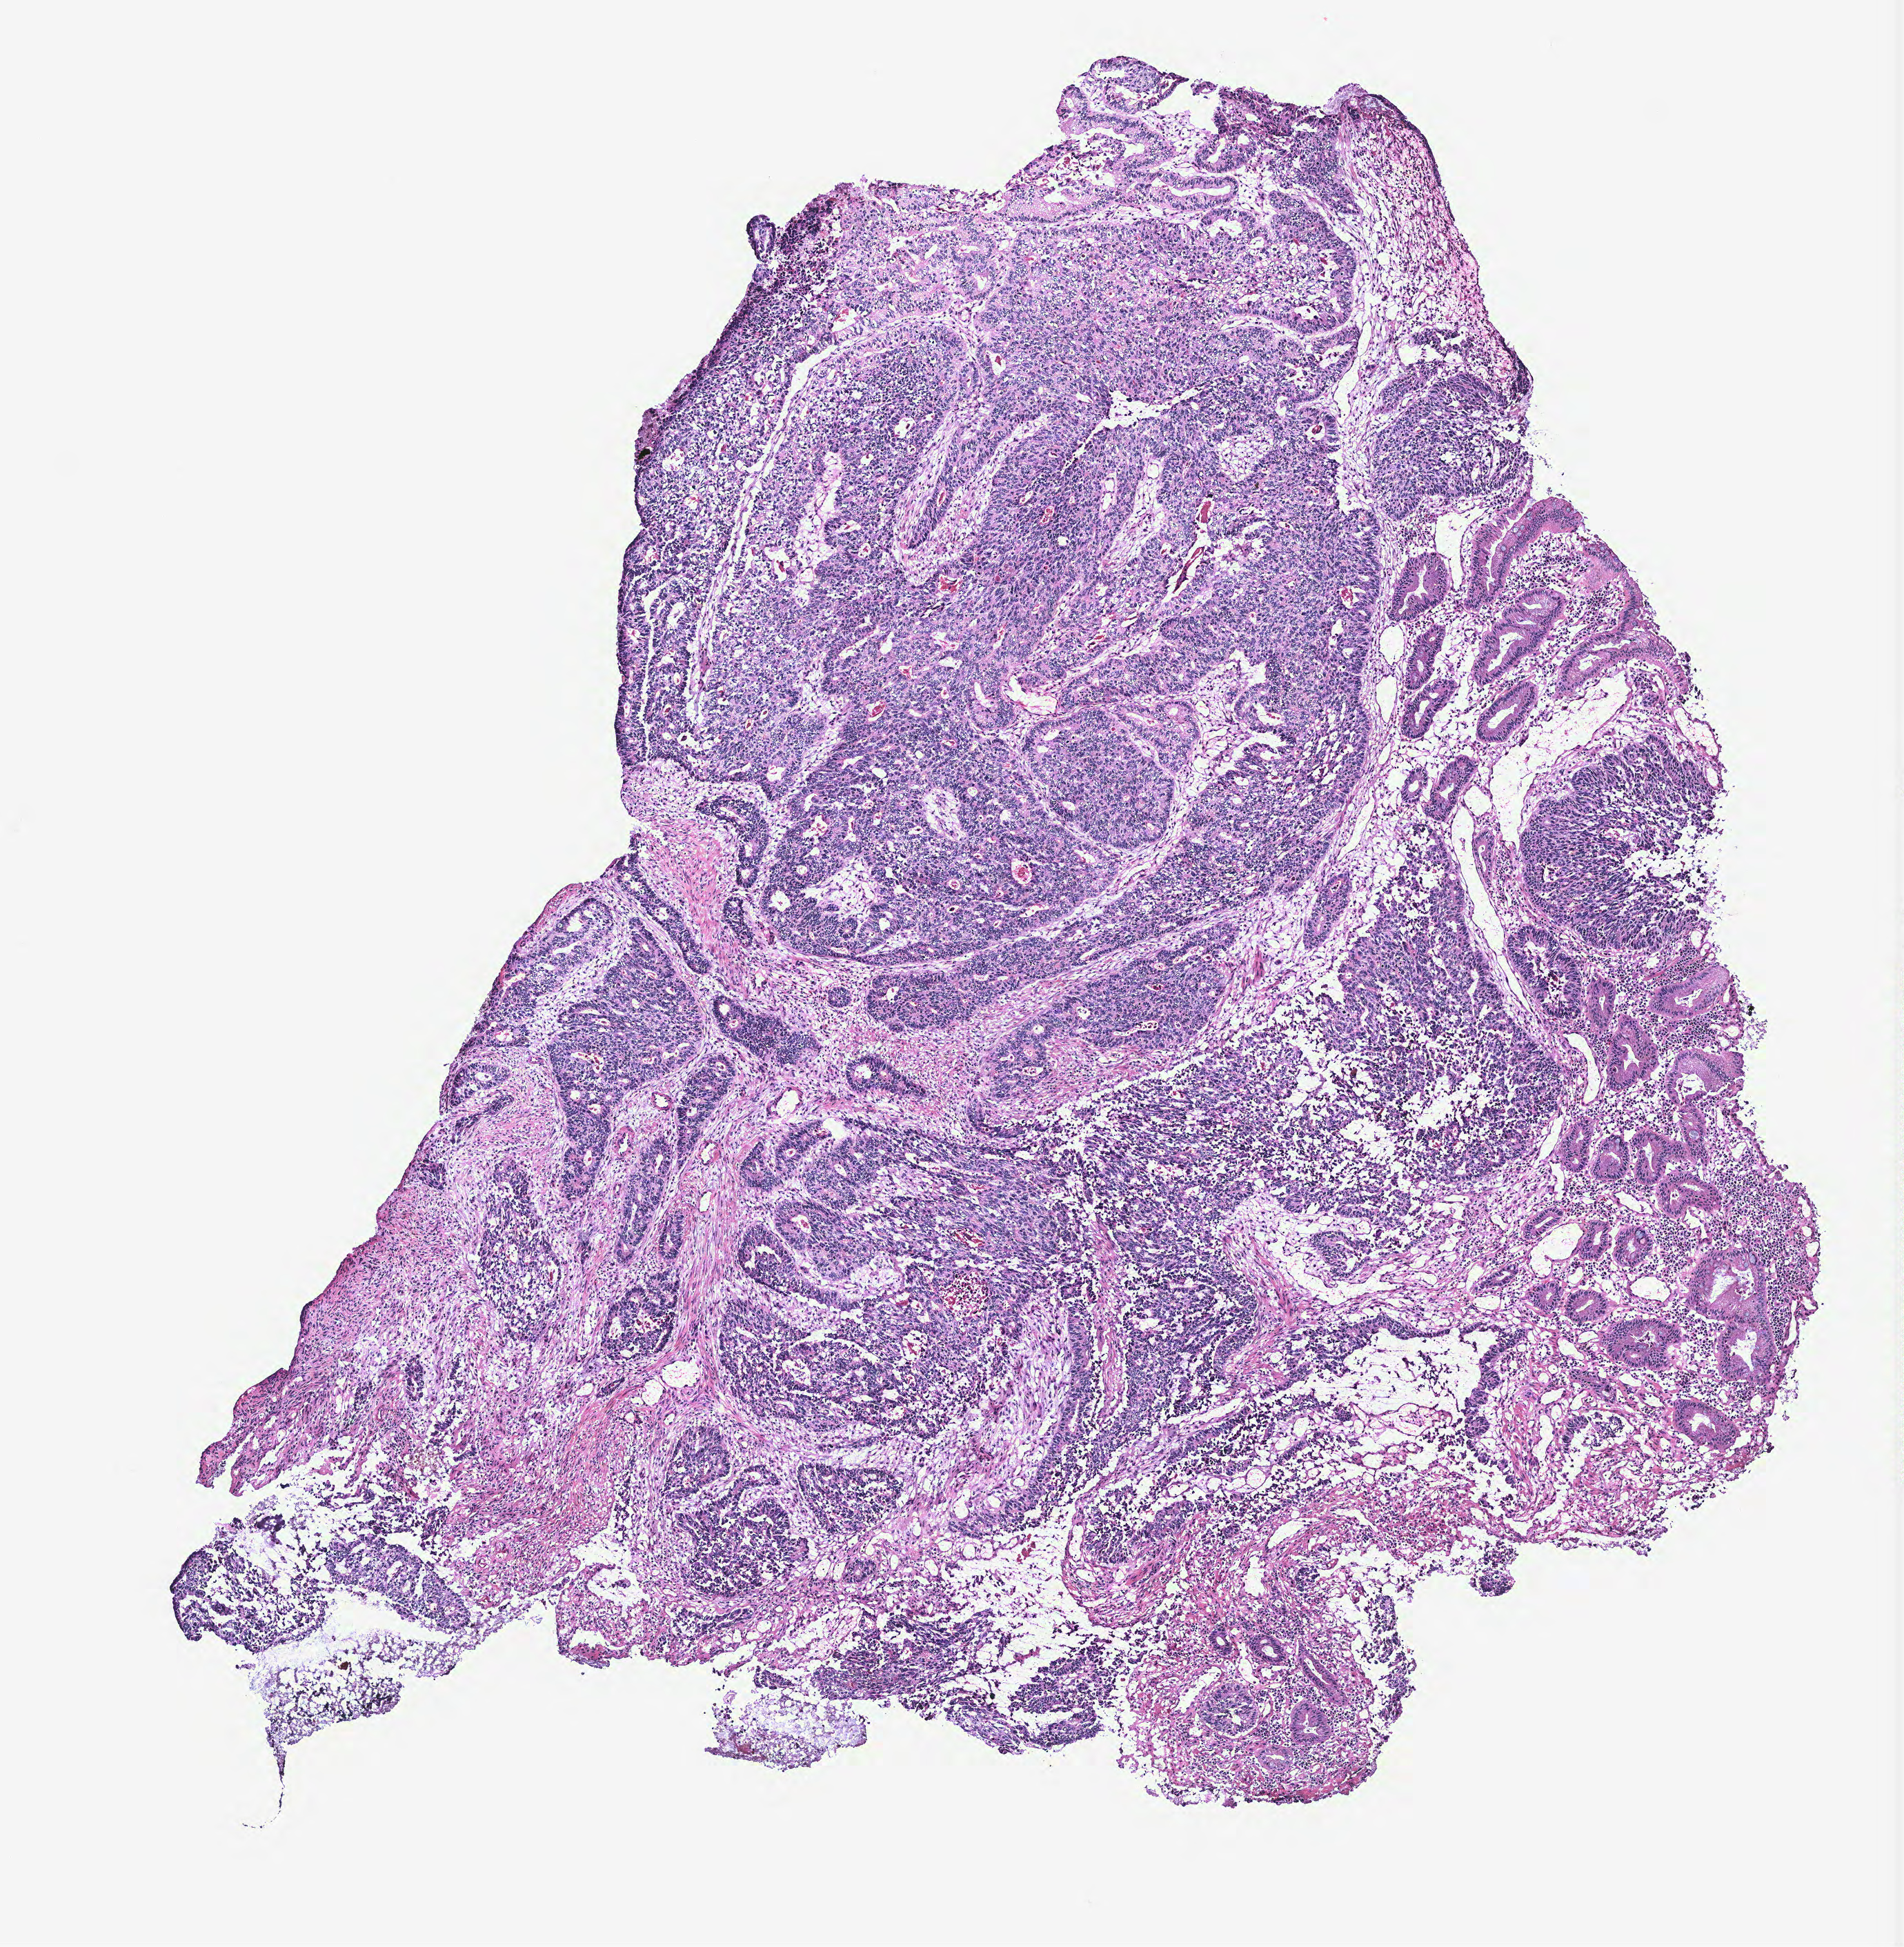
Whole-slide histology image, Hematoxylin and eosin (H&E) stained, shown as a low-resolution overview of the whole scanned area (about 5.5 x 5.6 mm), colon, tissue type not recorded.
Patient diagnosis (cohort enrolment): colon cancer (colon).